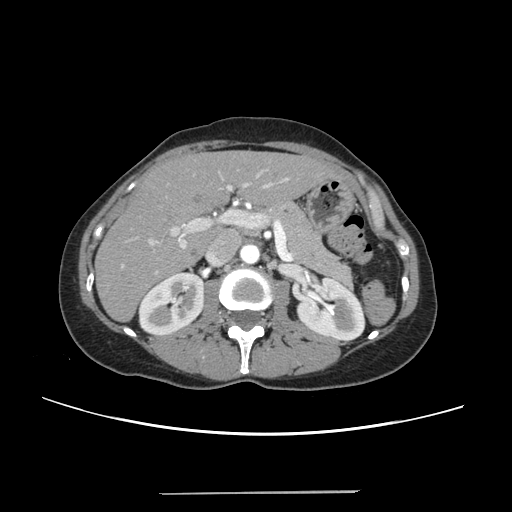
Contrast-enhanced abdominal CT, one axial slice. Position 132 of 240 along the scan axis. Soft-tissue window (W 400 / L 40 HU). 512 × 512 image matrix, field of view 371 × 371 mm. Female patient, age 60 years. From the clinical record (not read from this slice): diagnosis: colorectal cancer liver metastases, imaged before liver resection; multiple liver metastases: no; largest metastasis: 1.5 cm; disease in both lobes: no.
Outlined on this slice (manually delineated by an expert):
- liver: bounding box [x1, y1, x2, y2] px = [97, 152, 335, 320]
- planned liver remnant (the part of the liver to remain after resection): [97, 152, 334, 320]
- portal vein (with intrahepatic branches): [122, 172, 289, 274]